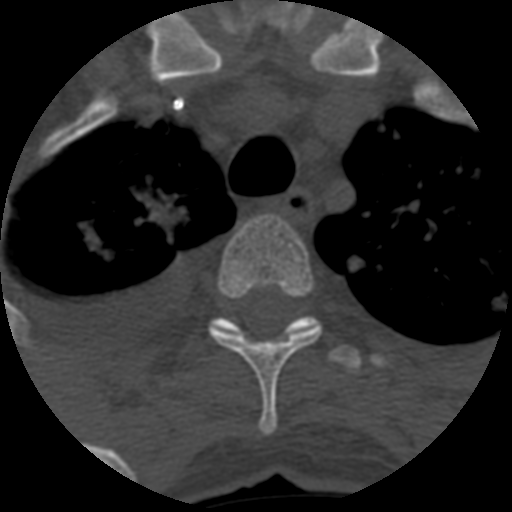
CT including the spine, one axial slice. Slice 484 of 708 in the series (ordered by position). Reconstruction kernel STANDARD. 120 kVp. One of 3 acquisitions stored at this slice position. Bone window (W 1800 / L 400 HU). 1.25 mm slice thickness. 512 × 512 image matrix, field of view 160 × 160 mm. Patient age 55 years. Case-level facts recorded for this patient, not image findings: primary cancer: colon; vertebrae with lytic lesions (as recorded): T12, L1, L5.
Annotated regions visible in this slice (semi-automatically segmented with operator editing):
- T3 vertebra: bounding box [x1, y1, x2, y2] px = [208, 215, 322, 435]
- T4 vertebra: [212, 316, 361, 373]